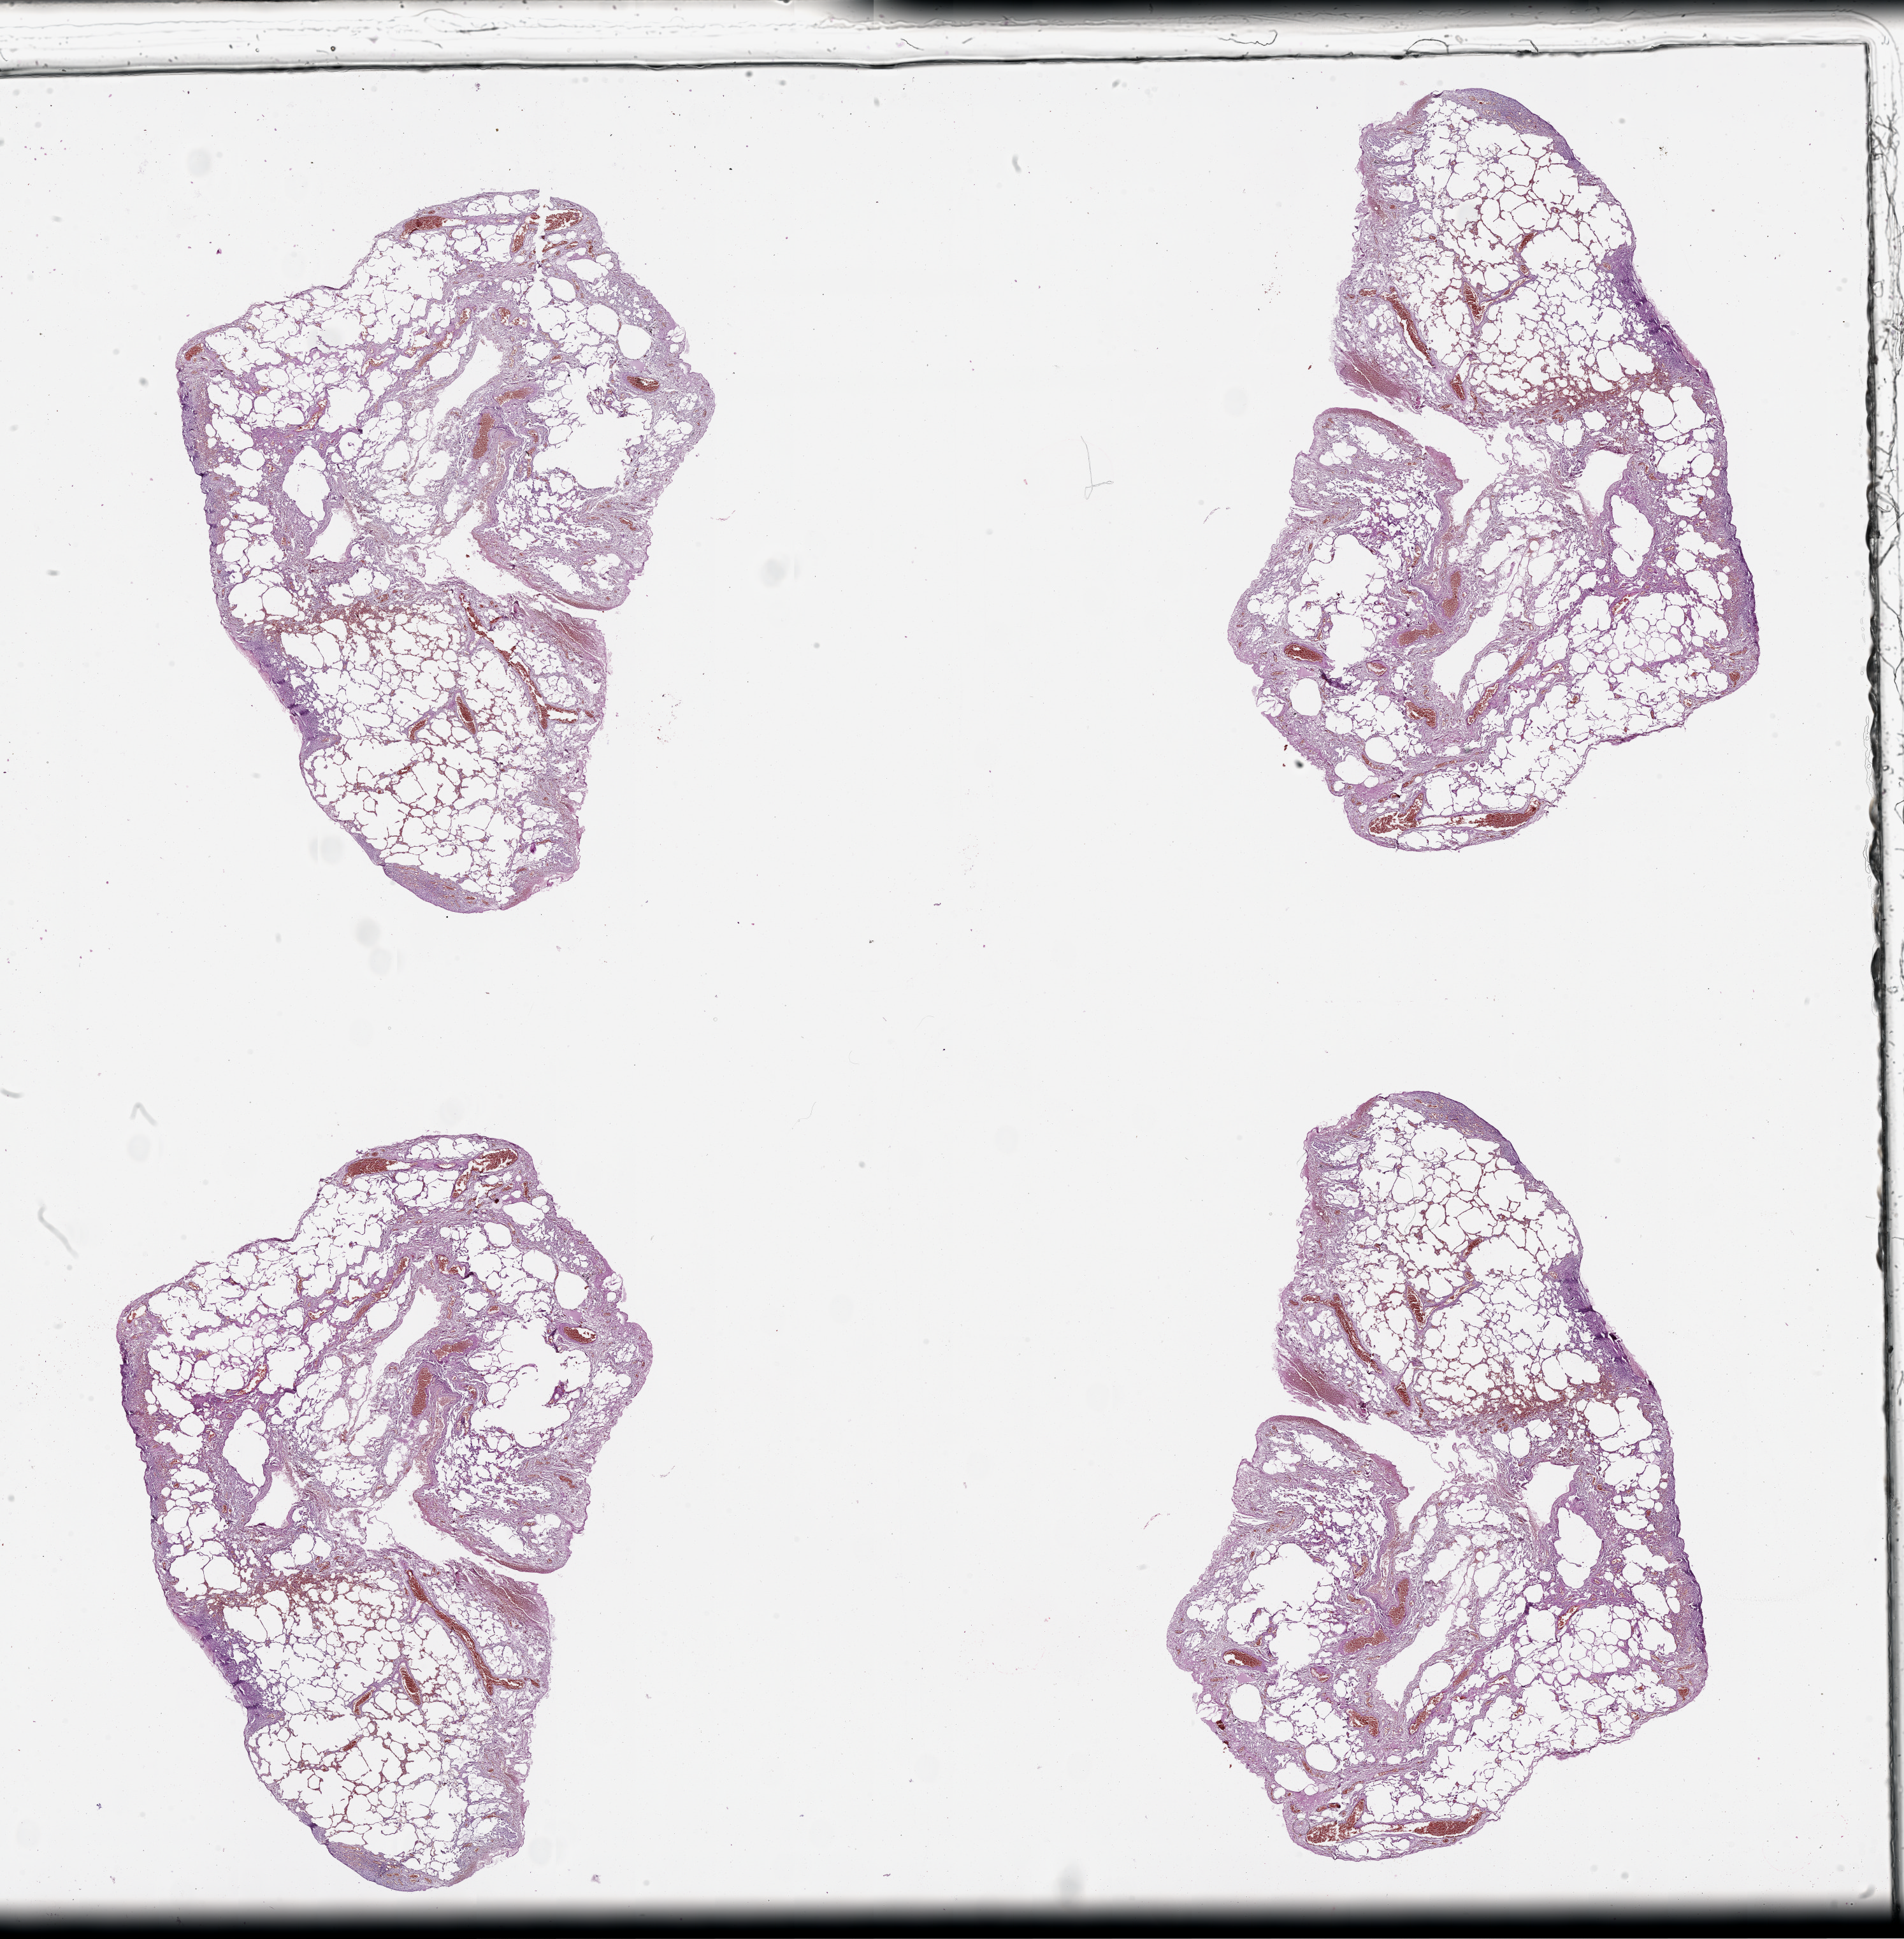
Digitized Hematoxylin and eosin (H&E) stained tissue section (whole slide), whole scanned area (about 24.1 x 24.5 mm, slide scanned at 20x) shown as a low-resolution overview. Lung, tissue type not recorded.
Patient diagnosis (cohort enrolment): lung adenocarcinoma (lung).